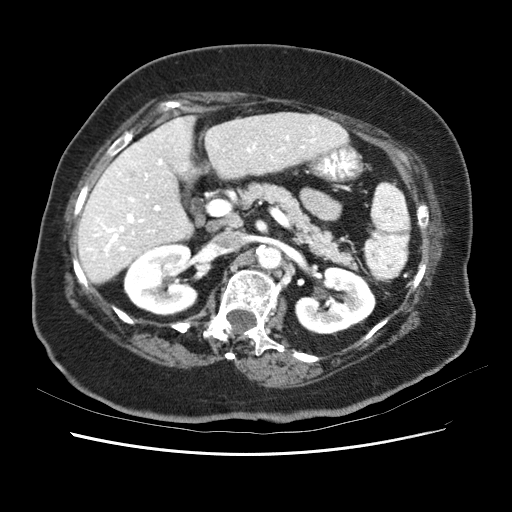
Contrast-enhanced abdominal CT (liver protocol), one axial slice; position 27 of 62 along the scan axis; reconstruction kernel STANDARD; soft-tissue window (W 400 / L 40 HU); 512 × 512 image matrix. Case-level facts recorded for this patient, not image findings: diagnosis: hepatocellular carcinoma (patient treated with transarterial chemoembolisation; whether this scan precedes or follows treatment is not stated here); TNM stage (as recorded): Stage-I; Child-Pugh class: B; tumour size: 5.3 cm.
Outlined on this slice (semi-automatically segmented with operator editing):
- liver parenchyma outside the tumour (the mass and vessels are separate outlines, so this box may not span the whole liver): box from (x=76, y=111) to (x=355, y=284) px
- liver vessels: (x=80, y=120)–(x=354, y=260)